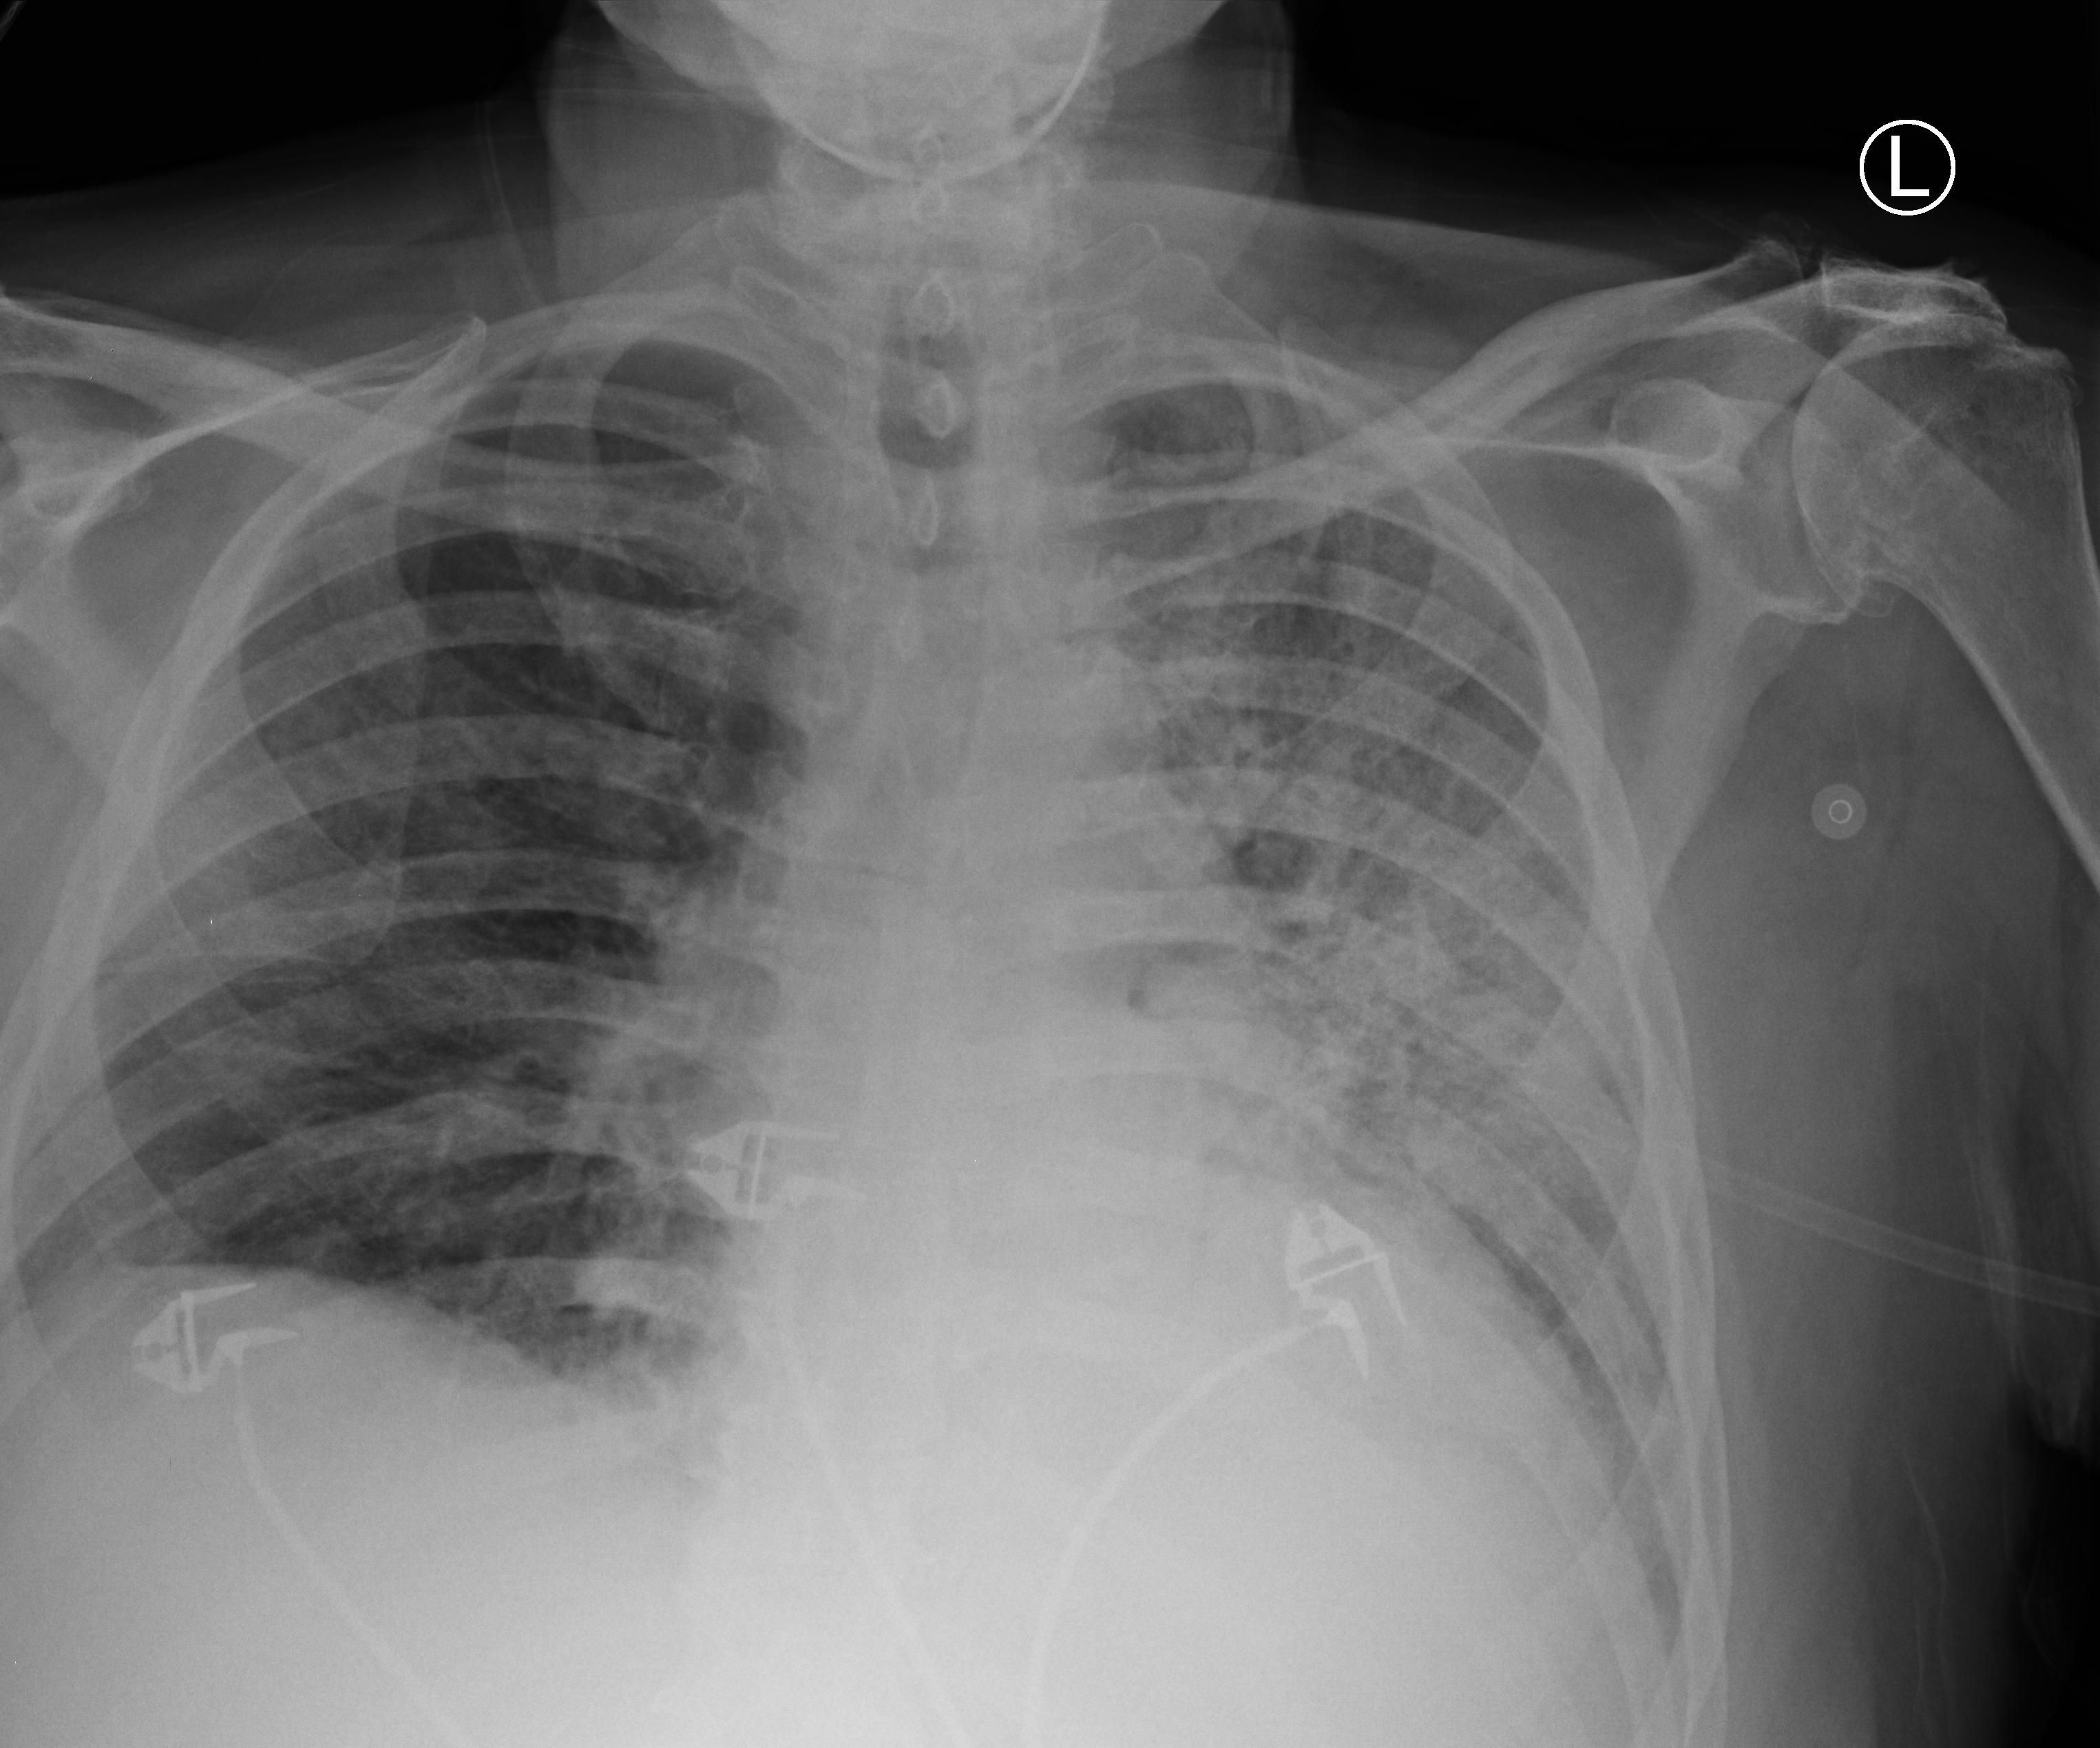
Portable chest radiograph; anteroposterior (AP) projection. Patient hospitalised with COVID-19; male, aged 60–74 years.
From the hospital-stay record, not from the radiograph (when in the stay this image was taken is not recorded): admitted to intensive care during this hospital stay: yes; mechanically ventilated during this hospital stay: yes; chronic kidney disease (admission record): no.